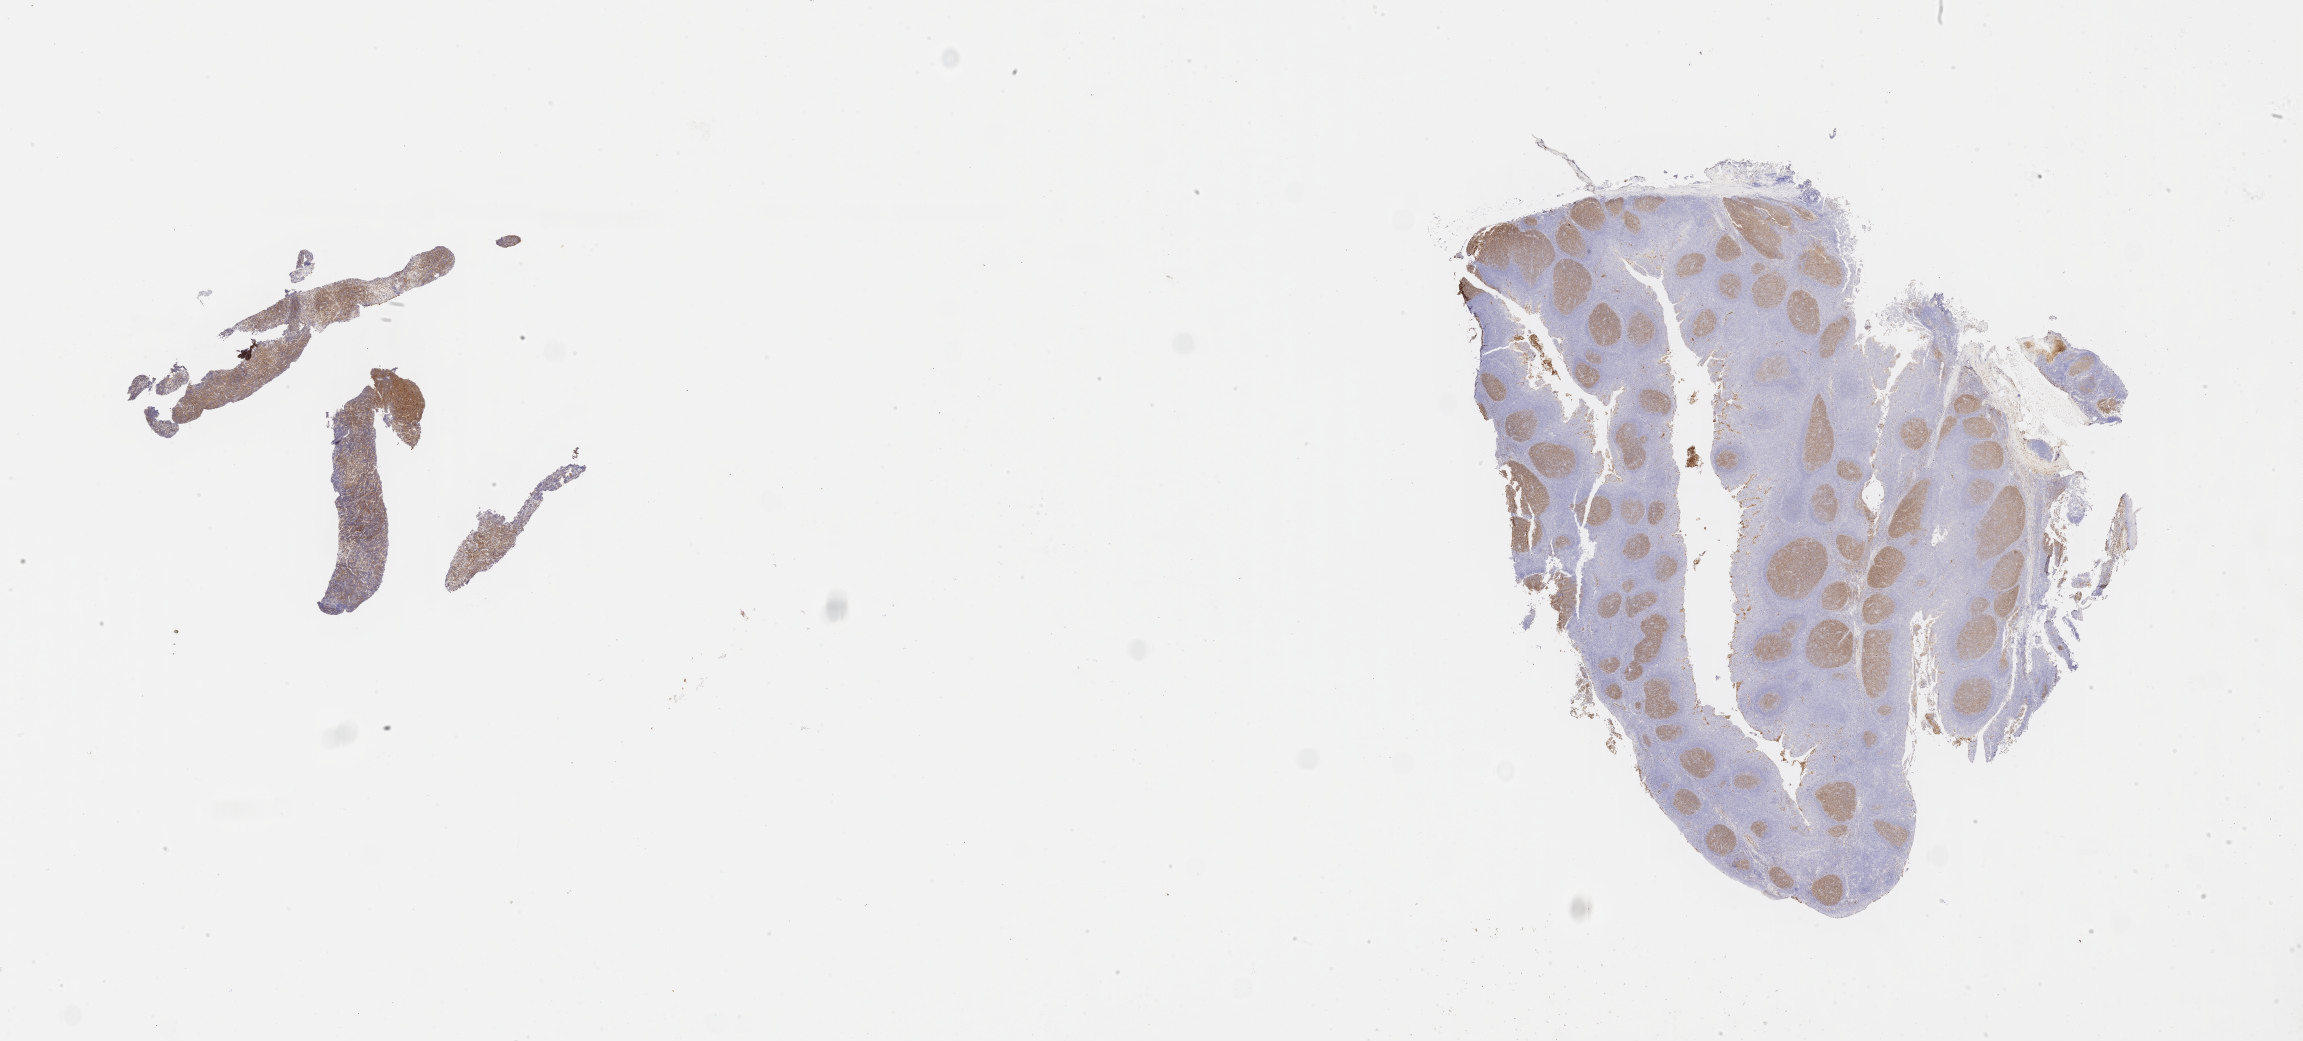
Whole-slide image, immunohistochemical stain for CD10, low-resolution overview of the scanned area, about 37.2 x 16.8 mm, tumor tissue, site: abdomen proper. Male, age 2 years at initial diagnosis.
Histologic diagnosis: Diffuse large B-cell lymphoma, NOS.